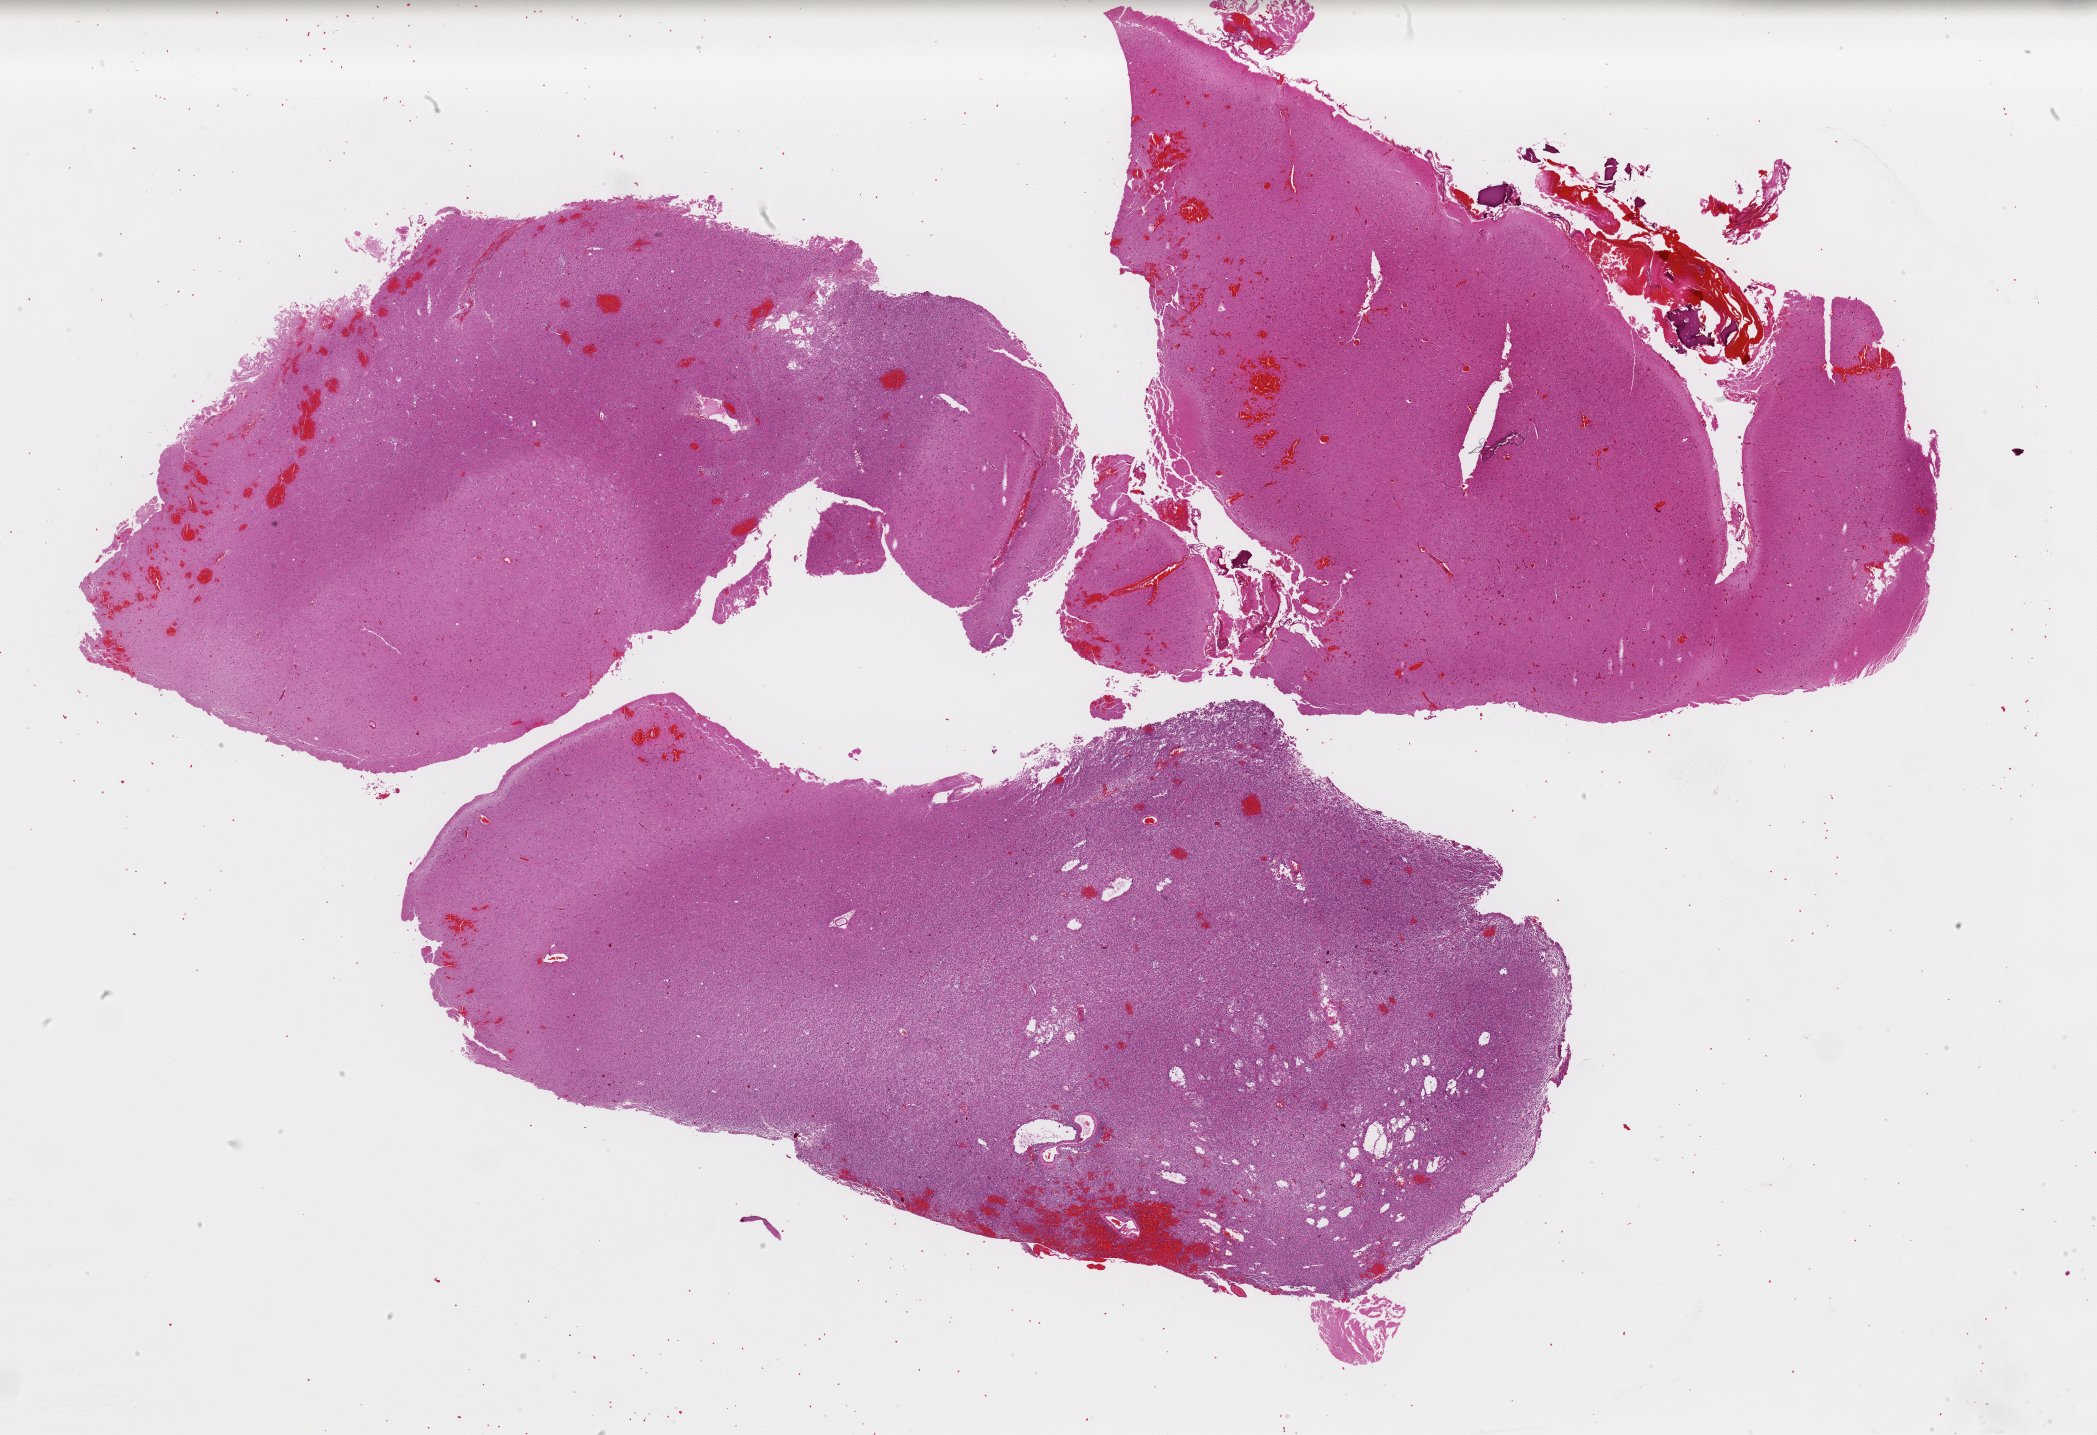
Whole-slide histology image, H&E-stained, a low-resolution overview of the entire scanned area, about 33.1 x 22.7 mm (slide scanned at 40x); formalin-fixed paraffin-embedded (FFPE) diagnostic section; sample: recurrent tumour, brain. Patient: female, age at initial diagnosis 27 years.
This section: recurrent tumour. Patient diagnosis: Oligodendroglioma, NOS (temporal lobe).